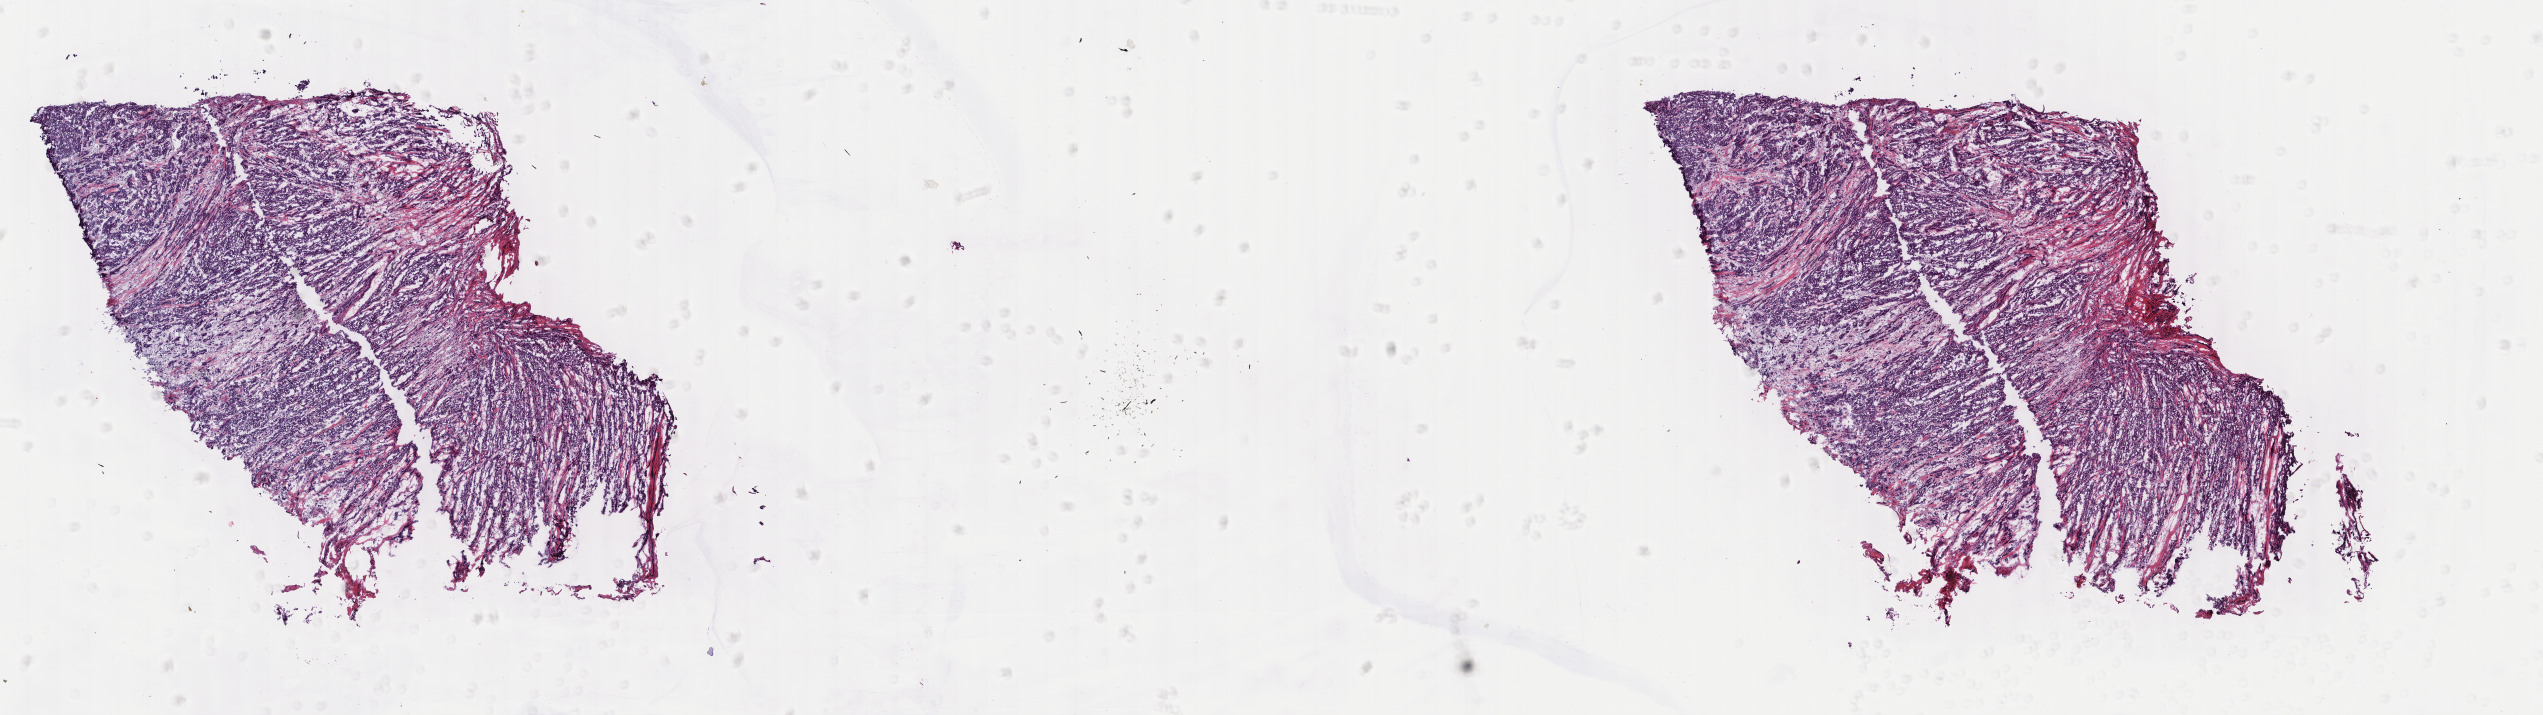
H&E whole-slide image, a low-resolution overview of the entire scanned area, about 20.2 x 5.7 mm; frozen section; primary tumour sample from the breast. Patient: female, age at initial diagnosis 62 years. Pathologist review of this section (percent, as recorded): tumour cells 65%, tumour nuclei 65%, normal cells 0%, stromal cells 32%, necrosis 3%. Inflammatory infiltration, as recorded: lymphocyte infiltration 15%, monocyte infiltration 1%, neutrophil infiltration 0%.
Laterality: right. AJCC pathologic stage: IA (6th edition). Histologic diagnosis: Infiltrating duct carcinoma, NOS. TNM: T1 N0 (i-) M0. Lymph nodes positive (case pathology): 0 of 1 examined.